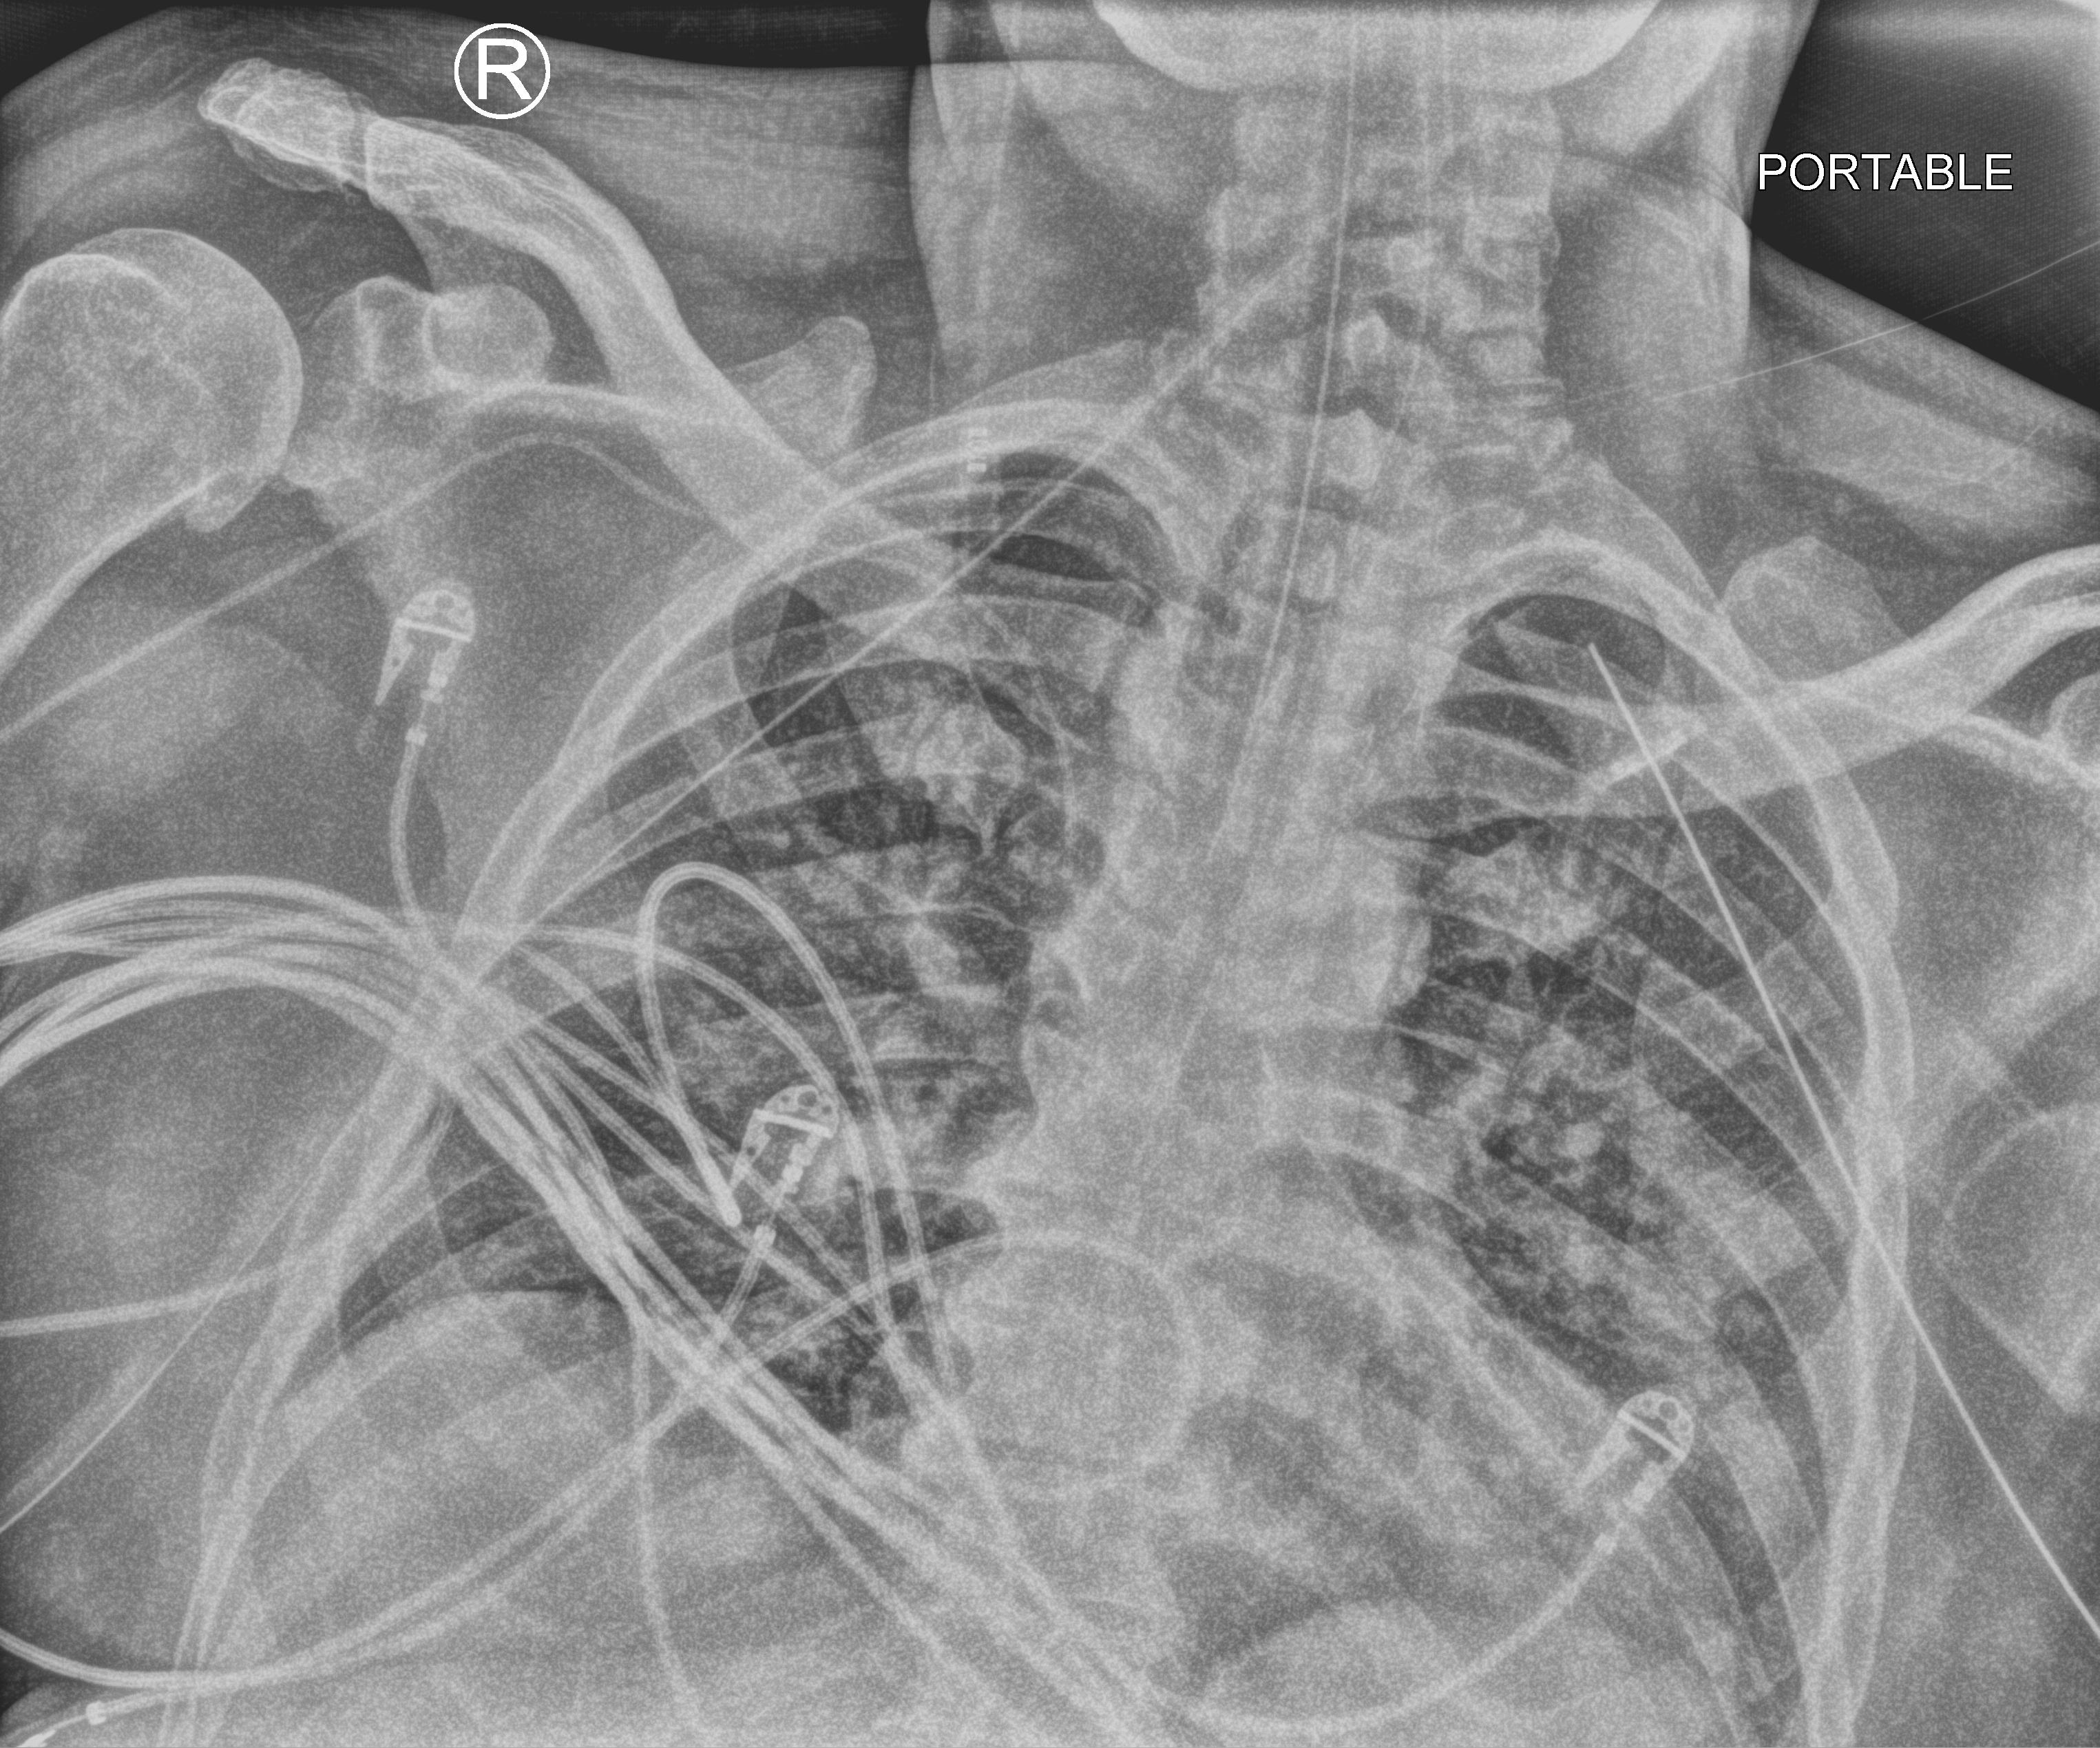
Bedside chest radiograph (computed radiography); anteroposterior (AP) projection. Patient hospitalised with COVID-19; male, aged 18–59 years.
Admission-level facts for this patient (not findings on this image; timing relative to this image not recorded):
- COPD (admission record): no
- chronic kidney disease (admission record): no